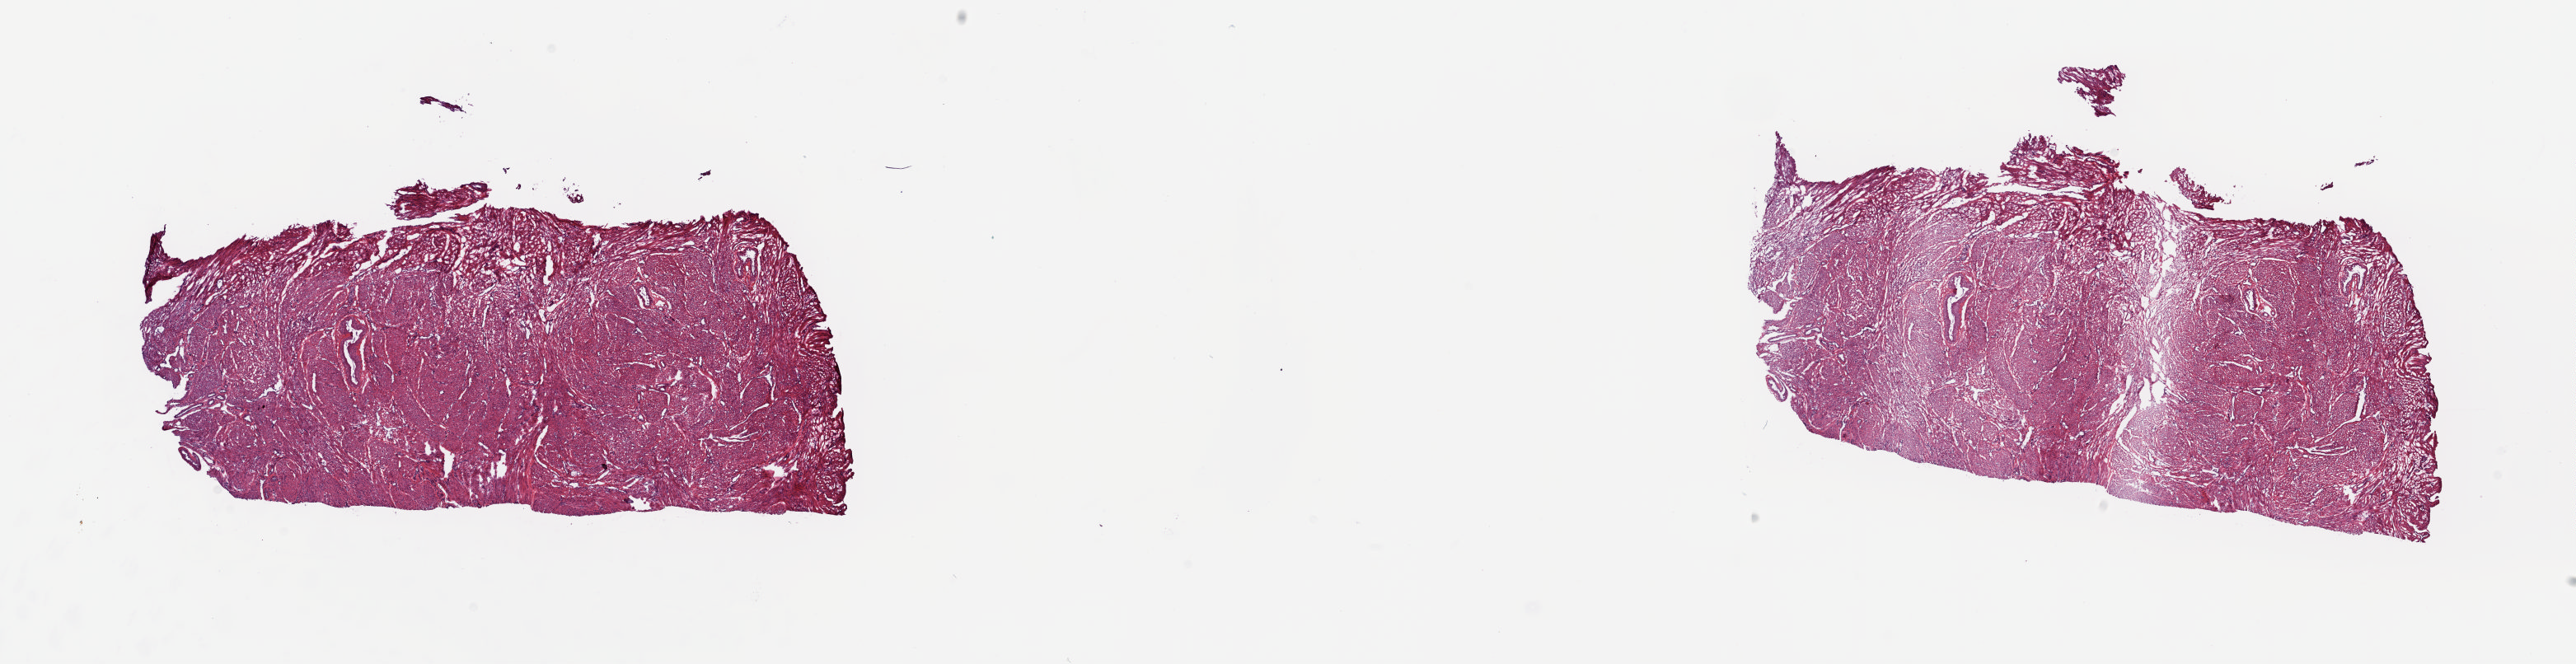
Whole-slide histology image, Hematoxylin and eosin (H&E) stained — a low-resolution overview of the entire scanned area, about 24.8 x 6.4 mm (slide scanned at 20x). Frozen section from the top of the tissue portion. Solid tissue normal (non-tumour tissue) sample from the cervix. Patient: female, age at initial diagnosis 44 years. Pathologist review of this section (percent, as recorded): tumour cells 0%, tumour nuclei 0%, normal cells 100%, stromal cells 0%, necrosis 0%. Inflammatory infiltration, as recorded: lymphocyte infiltration 0%, monocyte infiltration 0%, neutrophil infiltration 0%.
- this section: solid tissue normal sample (biorepository sample class)
- patient diagnosis: Squamous cell carcinoma, NOS